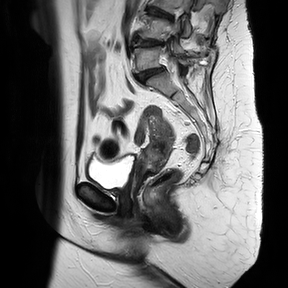
Pelvic MRI for cervical cancer, one sagittal slice; T2-weighted; 1.5 T; TE 100 ms, TR 4174.1 ms; 288 × 288 image matrix, field of view 300 × 300 mm. Female patient, age 65 years.
Outlined on this slice (manually delineated by an expert):
- uterus and cervix: box from (x=135, y=117) to (x=176, y=178) px